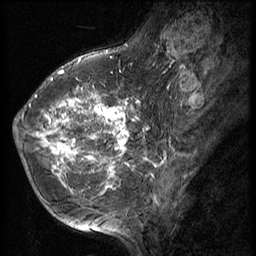
Breast MRI (dynamic contrast-enhanced), one sagittal slice. Position 21 of 56 along the scan axis. 3 images stored at this slice position (order not interpretable as contrast timing). 1.5 T. TE 4.2 ms, TR 9 ms. 2.5 mm slice thickness. 256 × 256 image matrix, field of view 180 × 180 mm. Female patient, age 49 years. Case-level facts recorded for this patient, not image findings: setting: breast cancer imaged before/during neoadjuvant chemotherapy; receptor status: HER2-positive.
Outlined on this slice (semi-automatically segmented with operator editing):
- analysis volume of interest (the breast-tissue region the enhancement analysis was run in; not a lesion): bounding box [x1, y1, x2, y2] px = [13, 79, 136, 203]
- tumour enhancement mask (voxels above the 140 % enhancement threshold inside the analysis volume of interest): [16, 83, 136, 190]